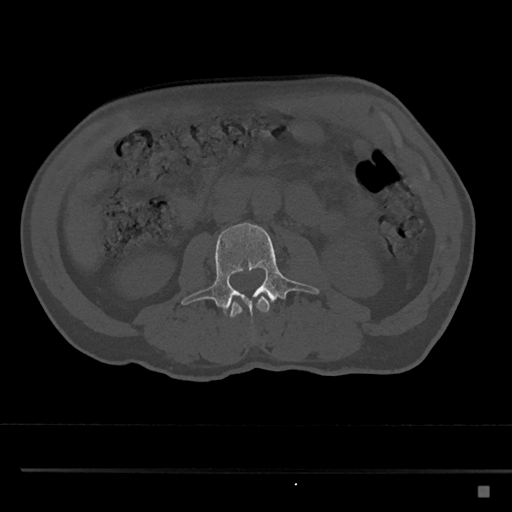
CT including the spine, one axial slice. Slice 708 of 797 in the series (ordered by position). Reconstruction kernel Br40s/3. 120 kVp. Bone window (W 1800 / L 400 HU). 0.5 mm slice thickness. 512 × 512 image matrix. Male patient, age 59 years. Case-level facts recorded for this patient, not image findings: primary cancer: prostate.
Structures marked on this image (semi-automatic segmentation, software-assisted and operator-edited):
- L2 vertebra: bounding box [x1, y1, x2, y2] px = [228, 296, 270, 318]
- L3 vertebra: [181, 222, 319, 334]